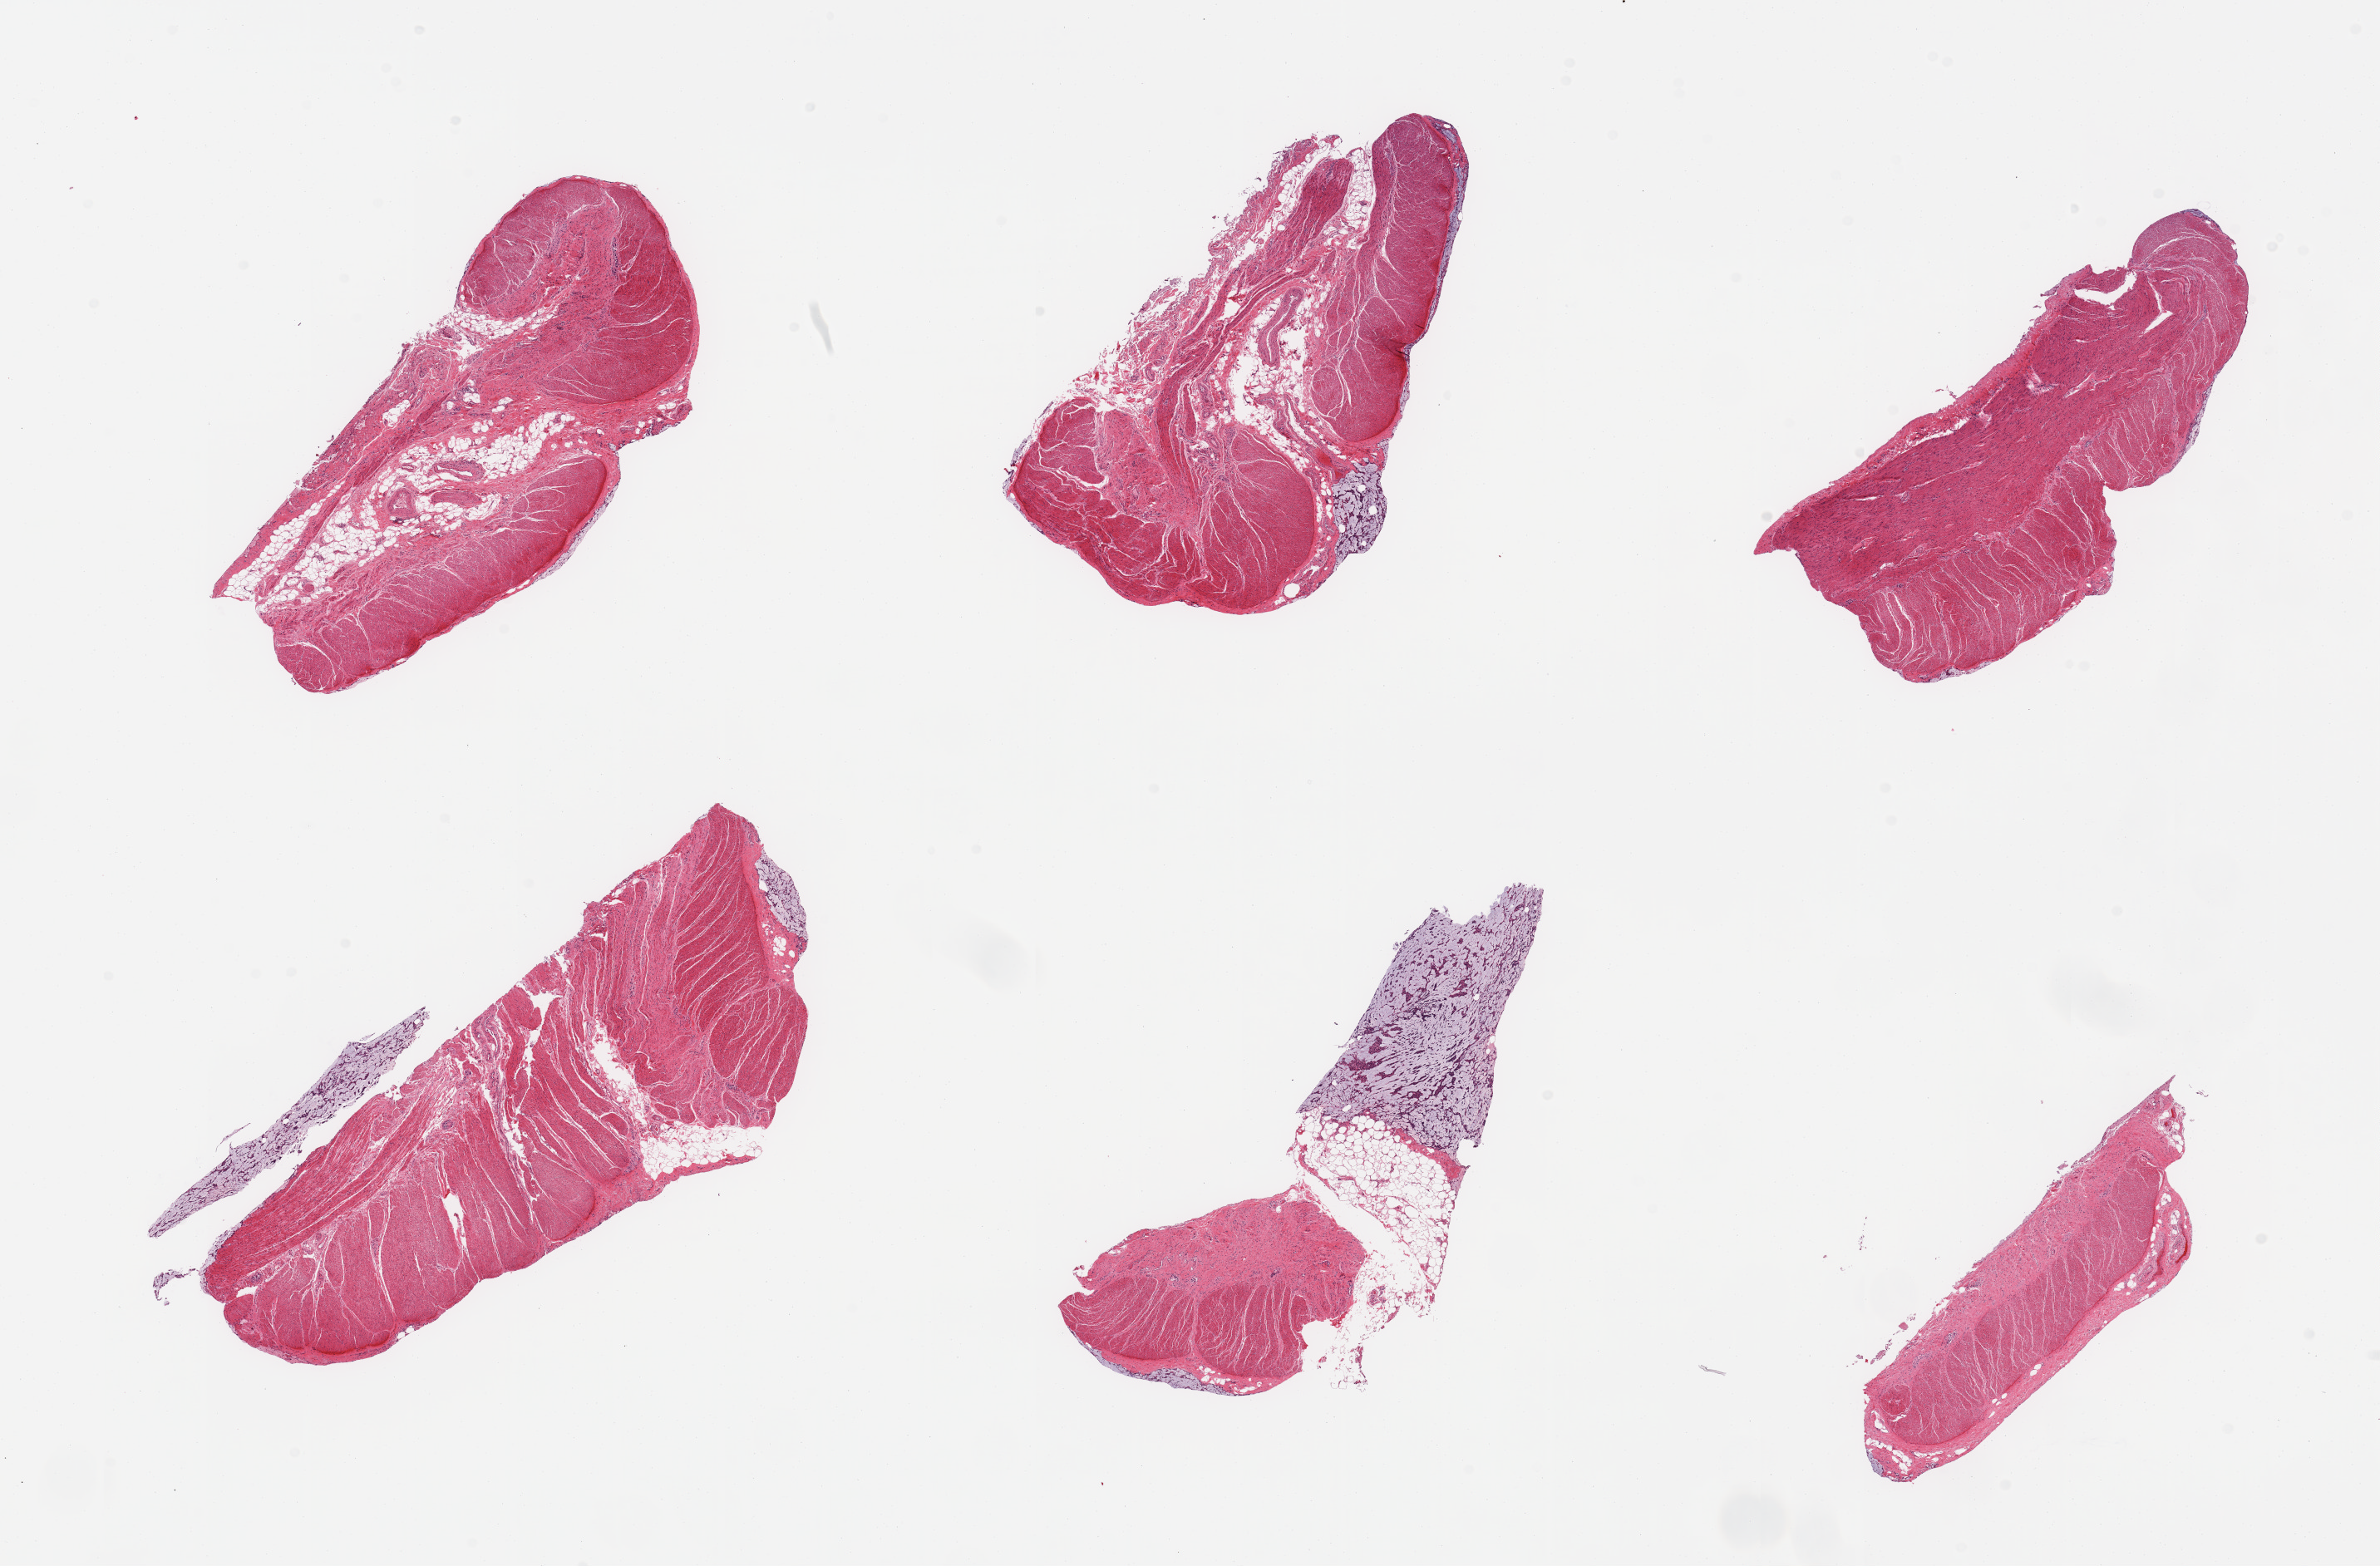
Digitized H&E-stained section, brightfield, whole scanned area (about 22.6 x 14.9 mm, from a 20x scan) shown as a low-resolution overview; PAXgene-fixed, paraffin-embedded tissue; sampled site (target tissue): sigmoid colon; donor tissue sample. Male donor.
Reviewer comment on this tissue sample: 6 pieces, confirmed target muscularis; few ~3mm nubbins of adherent fat/mucoid debris.